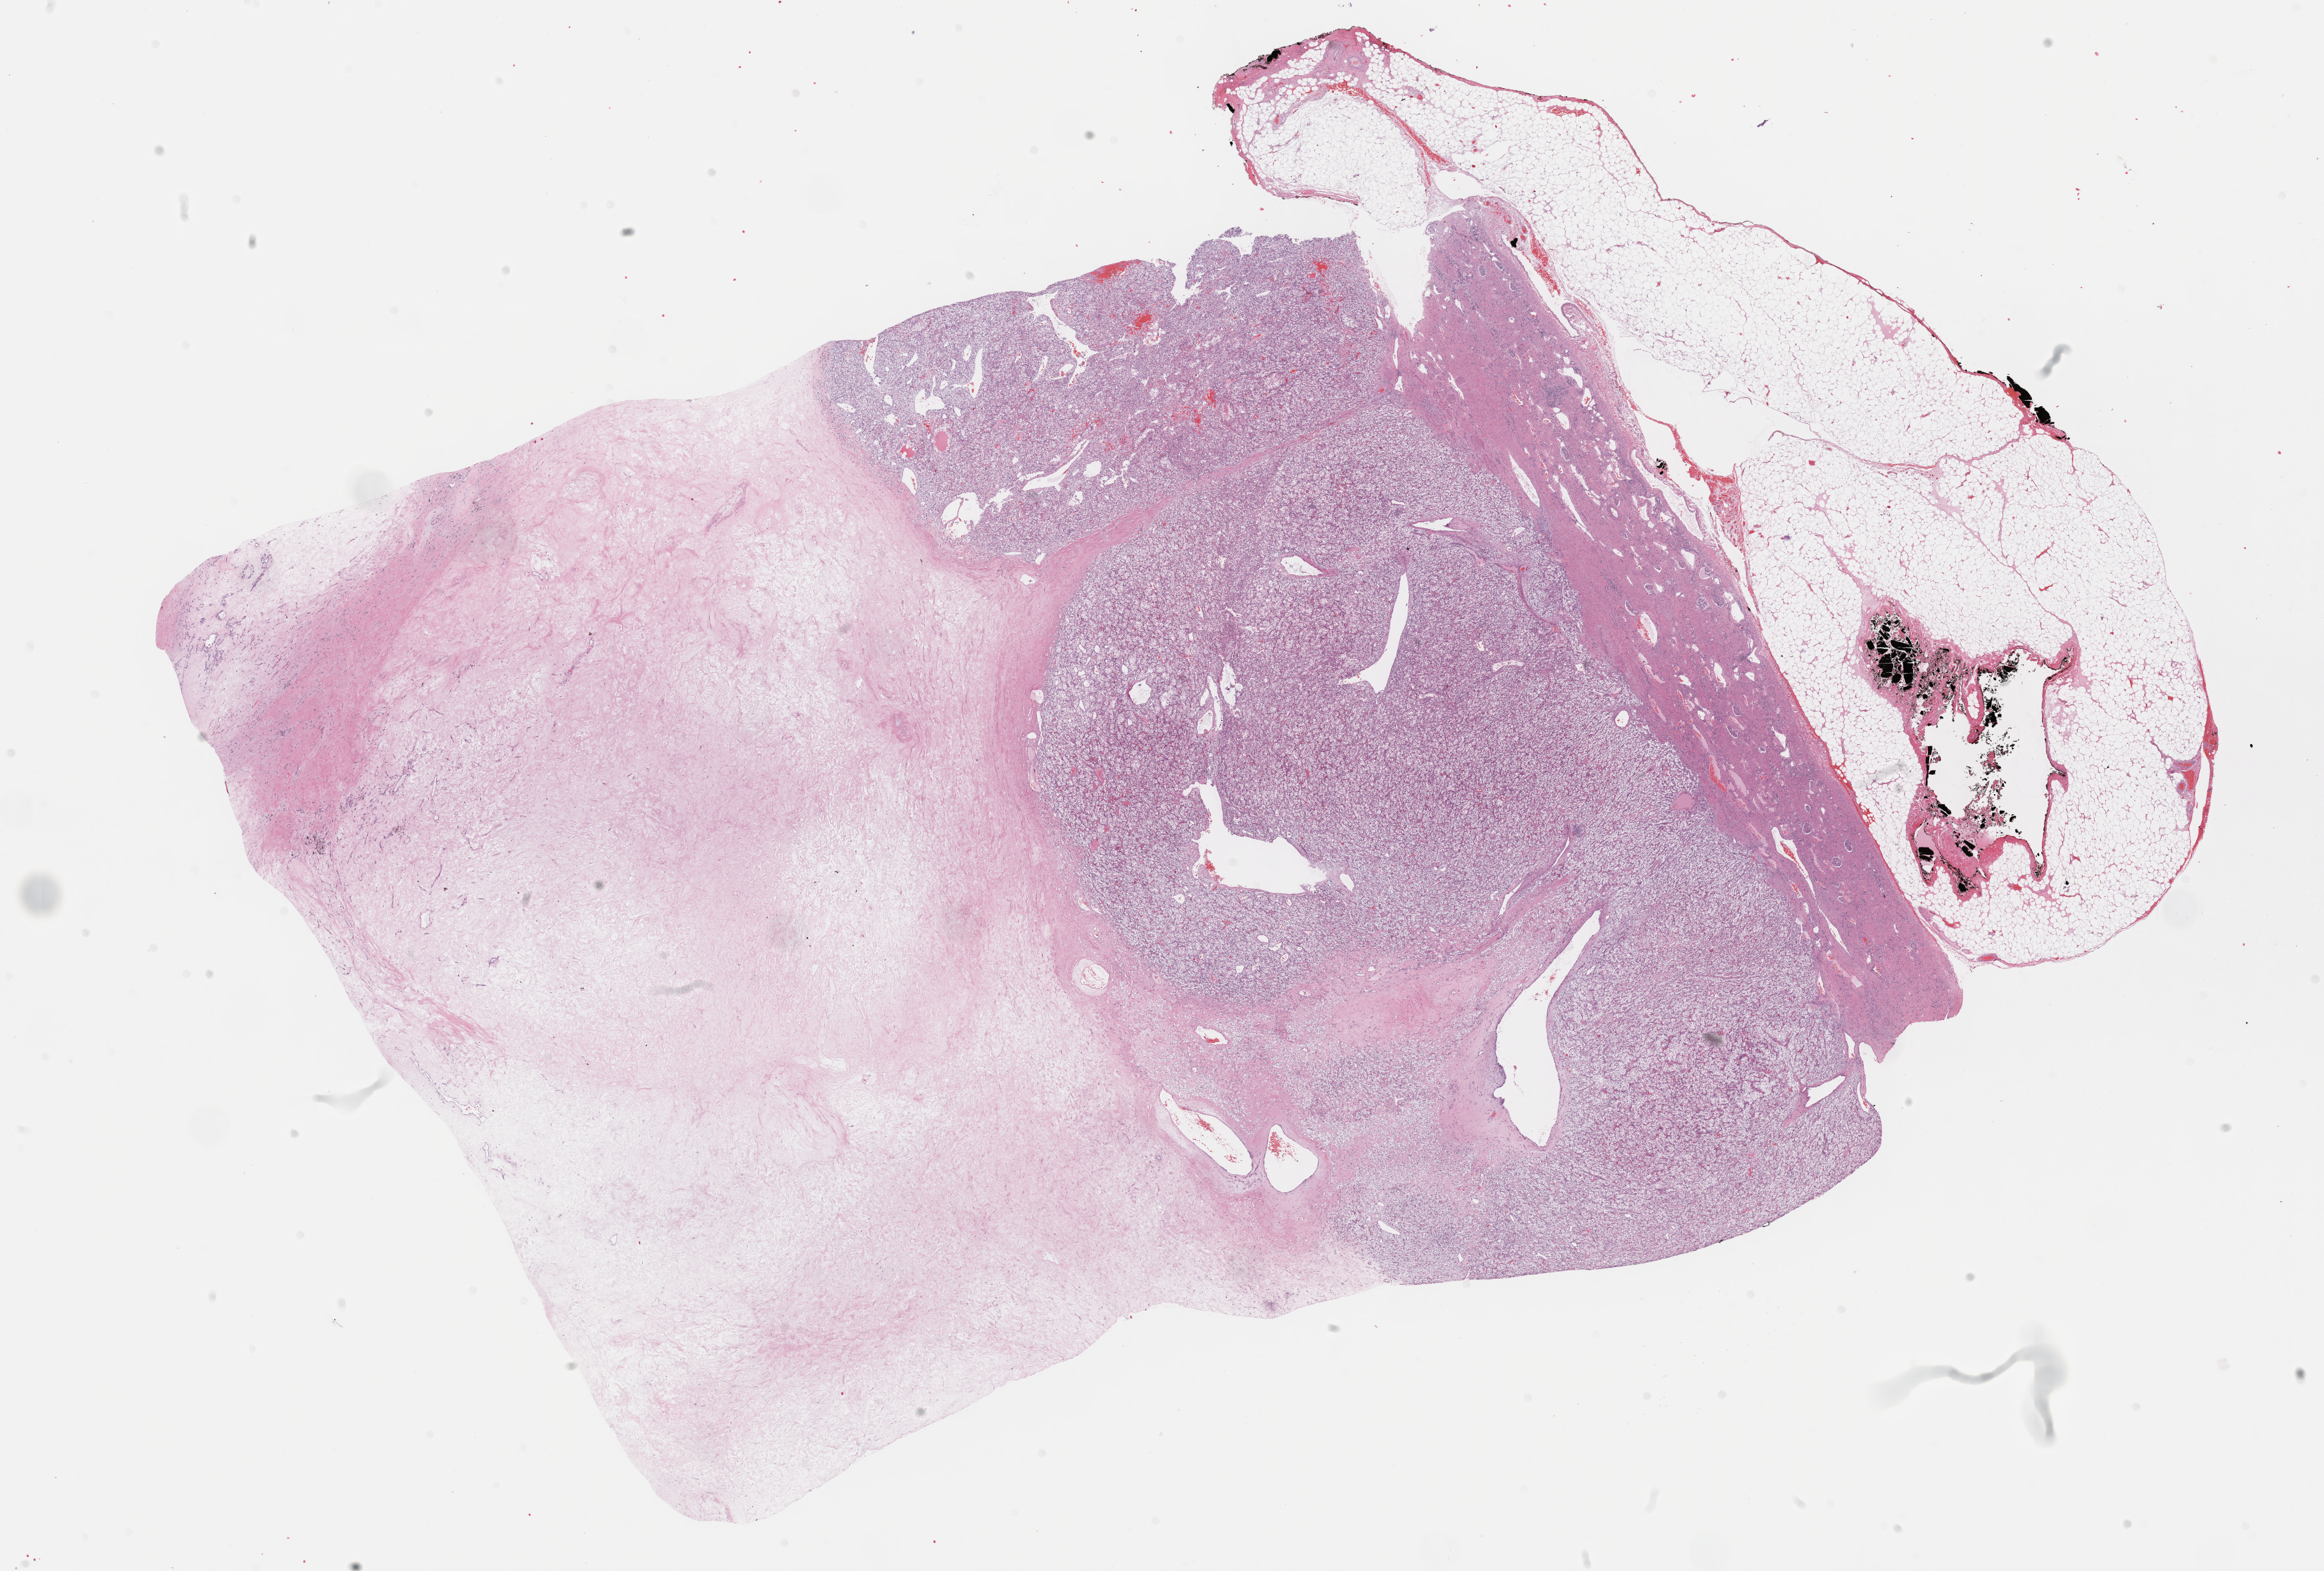
Whole-slide histology image, Hematoxylin and eosin (H&E) stained, whole scanned area (about 28.2 x 19.1 mm) shown as a low-resolution overview; formalin-fixed paraffin-embedded (FFPE) diagnostic section; kidney, primary tumour sample. Male patient; age at initial diagnosis 55 years. Histologic grade: G3 (poorly differentiated).
Histologic diagnosis: Clear cell adenocarcinoma, NOS. AJCC pathologic stage: IV.